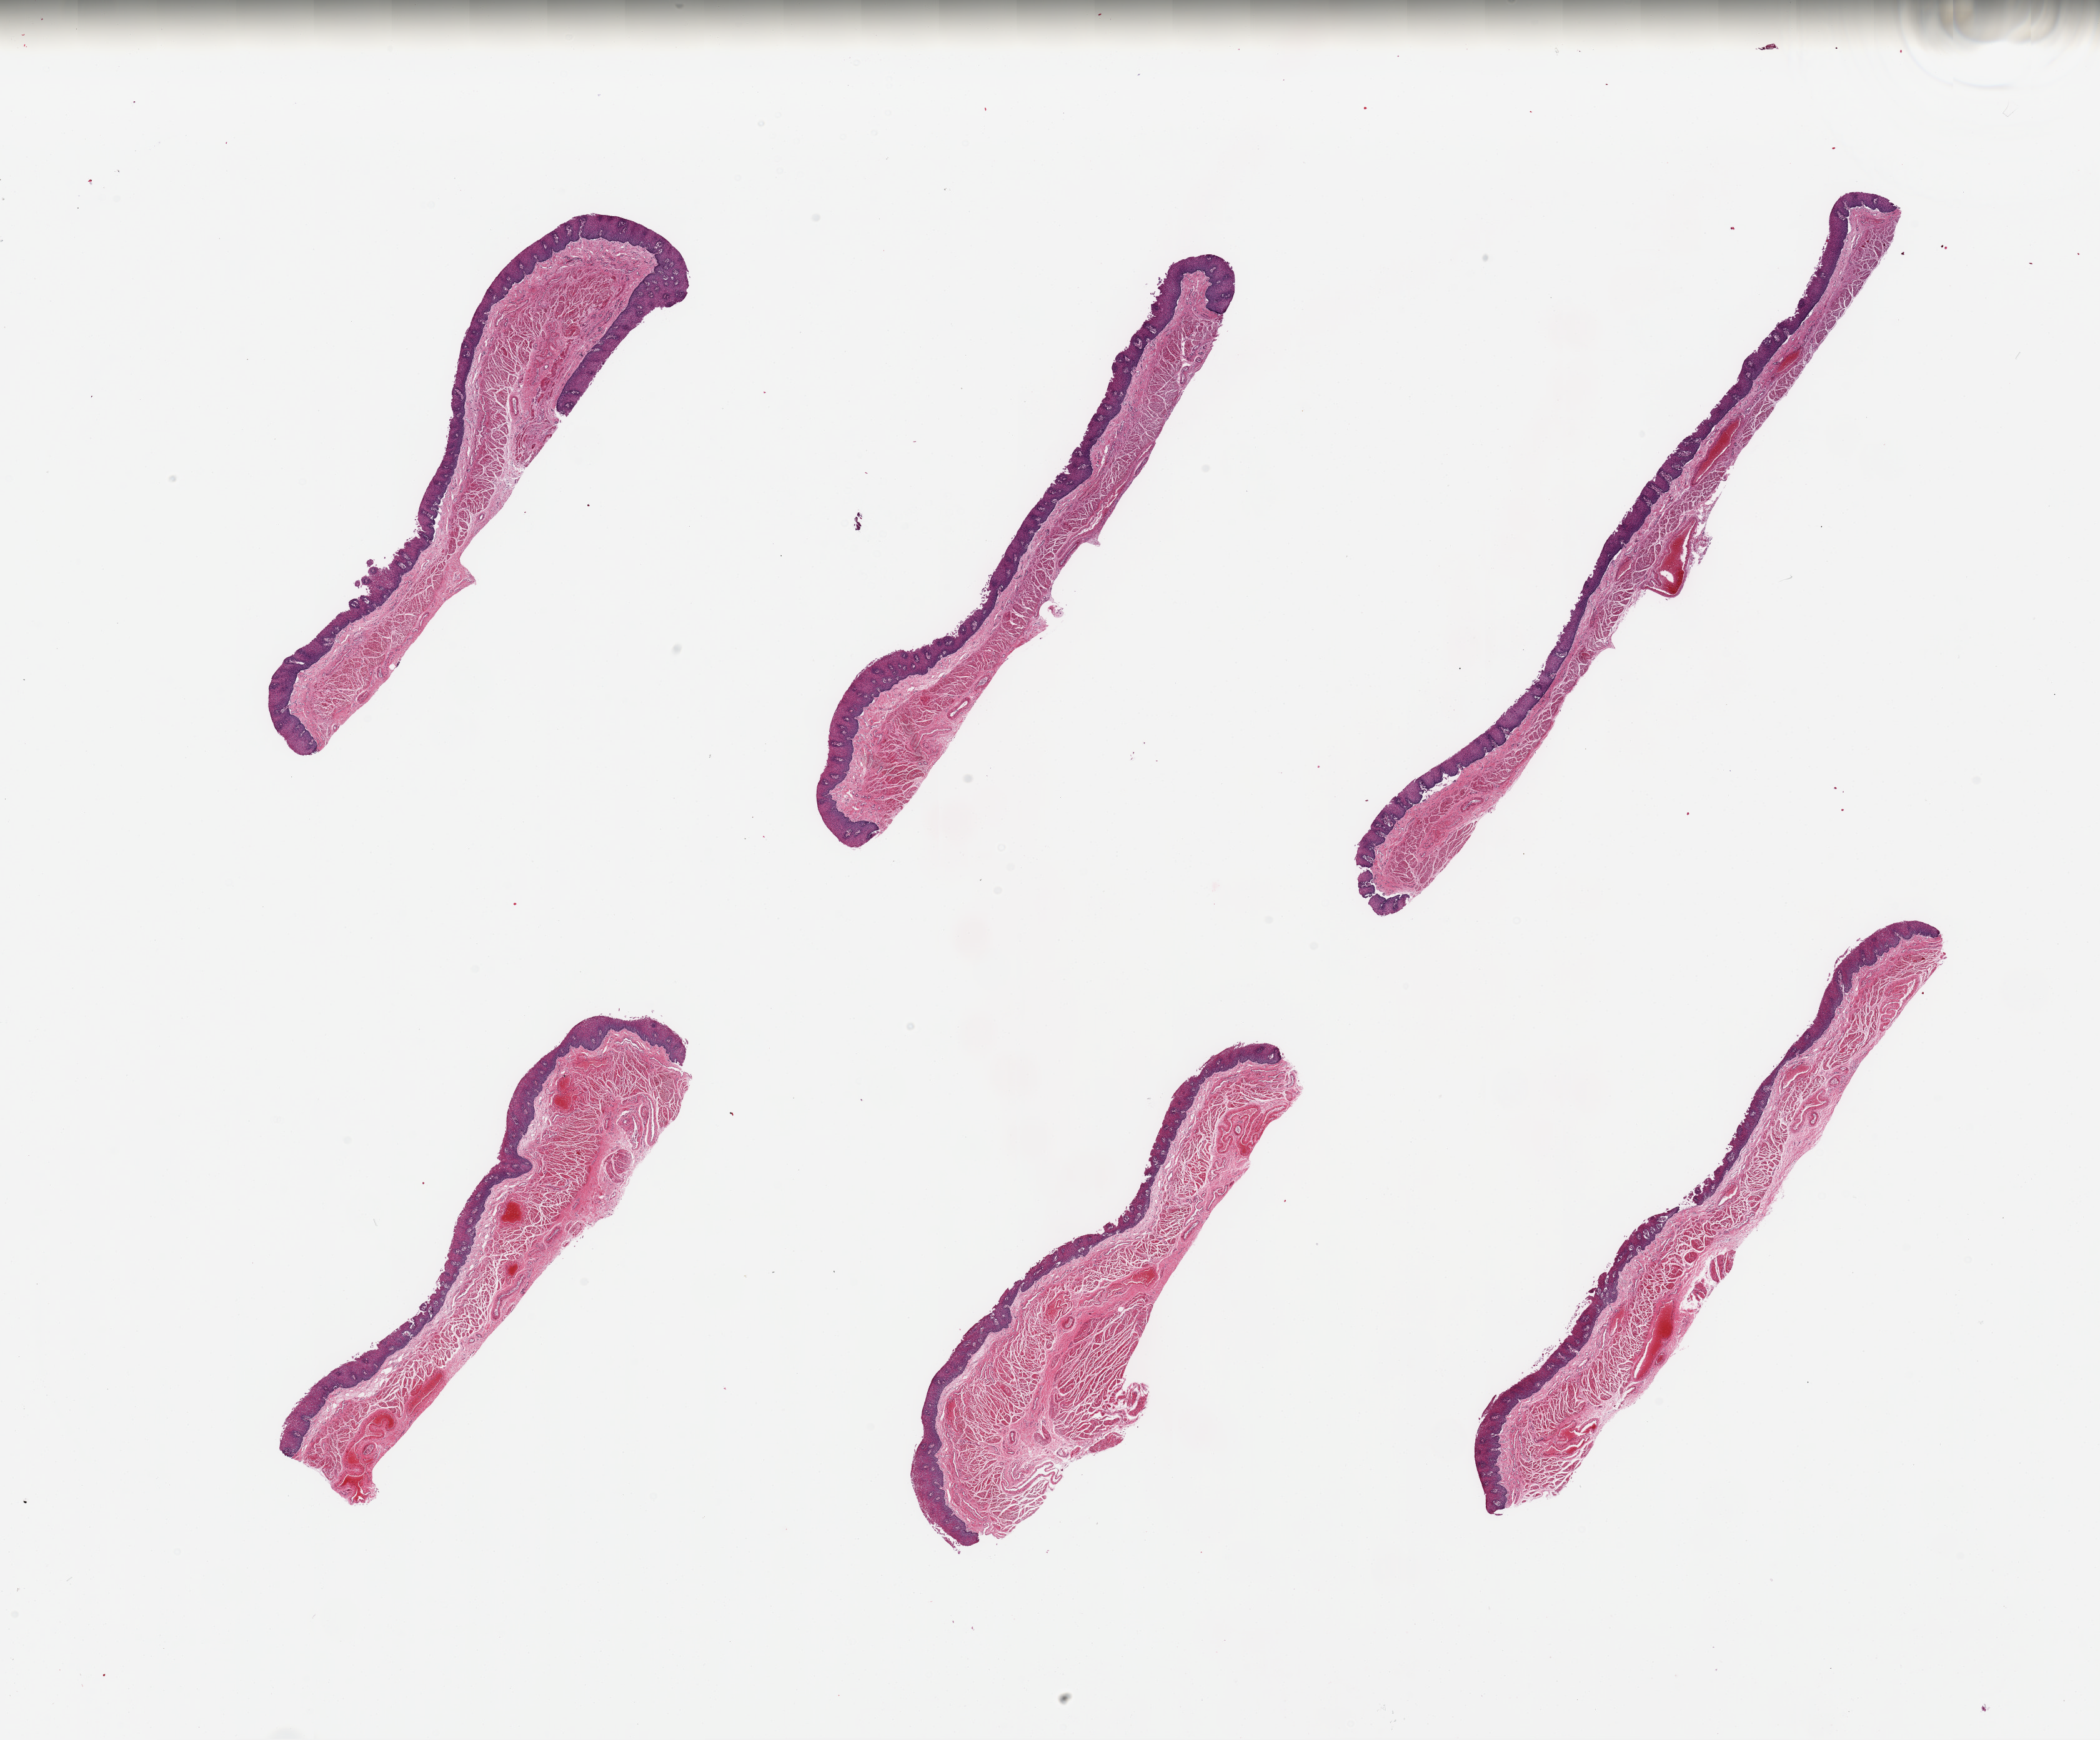
Whole-slide image, haematoxylin and eosin stain, brightfield, a low-resolution overview of the entire scanned area, about 26.6 x 22.0 mm (slide scanned at 20x), PAXgene-fixed, paraffin-embedded tissue, section of esophageal mucous membrane (target tissue), tissue donor sample. Donor sex: female.
• pathologist's review note for this sample: 6 pieces; well dissected mucosa; focally sloughed mucosa